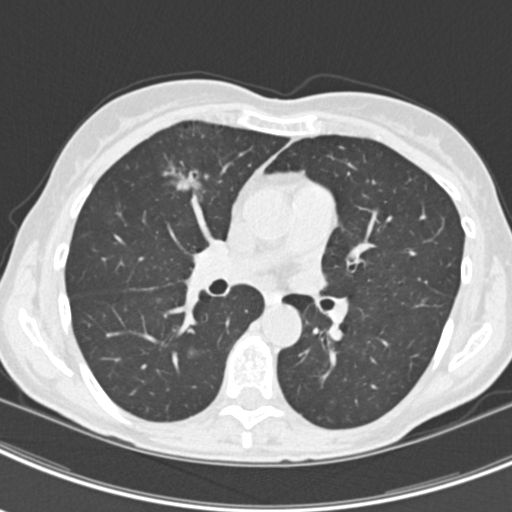
Low-dose screening chest CT, axial slice, second screening round (one year after baseline), lung window (W 1500 / L -600 HU), 2 mm slice thickness, slice 89 of 219 in the series, 512 × 512 image matrix. Female participant, aged 63 years at enrolment. Current smoker at enrolment.
Lesion marked by an expert reader, box from (x=161, y=152) to (x=221, y=204) px. The screening reader recorded 9 non-calcified nodules or masses ≥4 mm on this exam (left upper lobe, right upper lobe, left upper lobe, left lower lobe, right middle lobe, left lower lobe, left lower lobe, right lower lobe, right lower lobe); which of them this box marks is not recorded. Official screen result: positive, other. Participant outcome: lung cancer diagnosed 408 days after this screen (after the third annual screen) — bronchiolo-alveolar adenocarcinoma, NOS, right upper lobe, right middle lobe, right lower lobe, left upper lobe, left lower lobe, moderately differentiated (G2), stage IV (AJCC 6th edition).